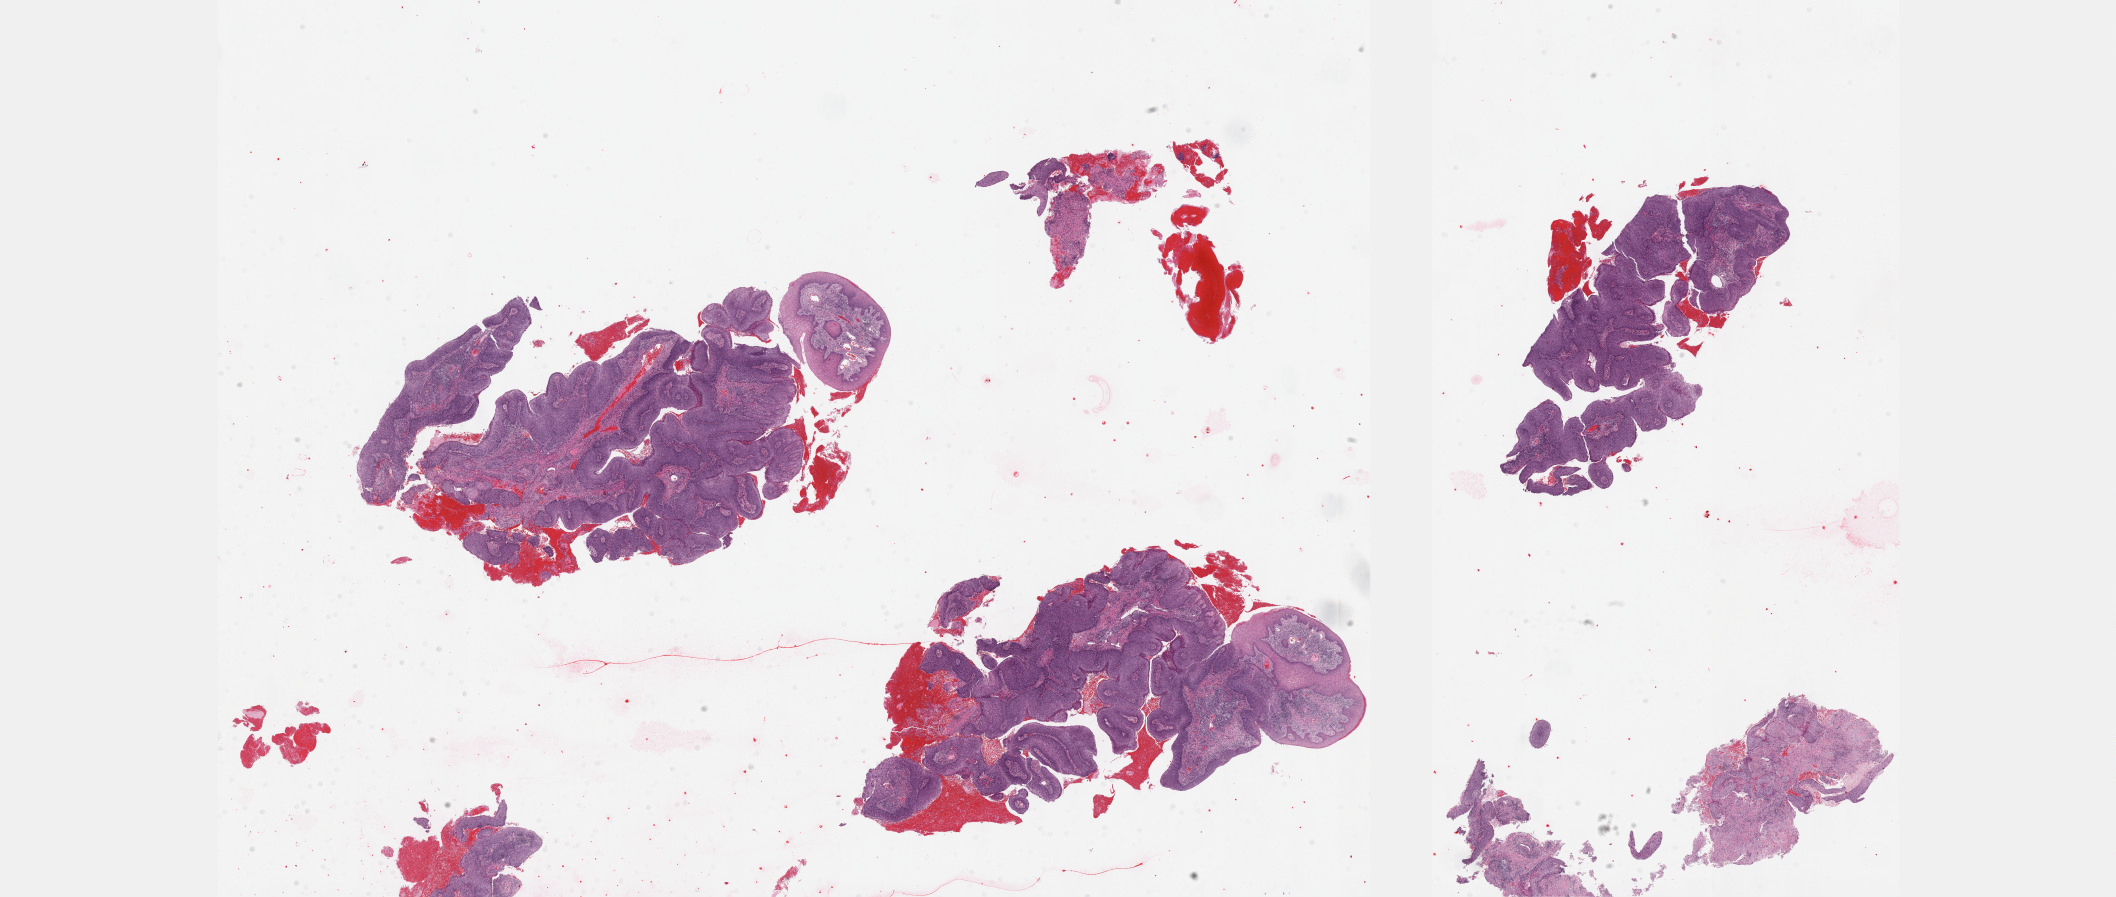
Hematoxylin and eosin (H&E) stained whole-slide image, low-resolution overview of the scanned area, about 34.2 x 14.5 mm (acquisition: 40x scan). Formalin-fixed paraffin-embedded (FFPE) diagnostic section. Sample: primary tumour, cervix. Patient: female, age at initial diagnosis 44 years. Histologic grade: GX (grade cannot be assessed).
Diagnosis: Squamous cell carcinoma, large cell, nonkeratinizing, NOS (cervix uteri). FIGO stage: I.